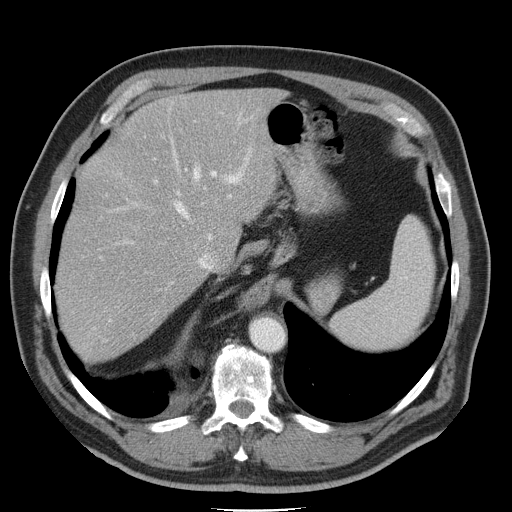
Contrast-enhanced abdominal CT, one axial slice. Slice 35 of 45 in the series (ordered by position). 120 kVp. Intravenous contrast given. Soft-tissue window (W 400 / L 40 HU). 512 × 512 image matrix, field of view 386 × 386 mm. Male patient, age 65 years. Case-level facts recorded for this patient, not image findings: diagnosis: colorectal cancer liver metastases, imaged before liver resection; multiple liver metastases: yes; largest metastasis: 4.9 cm; disease in both lobes: no.
Structures marked on this image (outlined manually by an expert reader):
- hepatic veins: bounding box <82,137,214,337> (left, top, right, bottom; pixels)
- liver: <58,89,278,358>
- planned liver remnant (the part of the liver to remain after resection): <105,89,278,260>
- portal vein (with intrahepatic branches): <130,148,251,232>